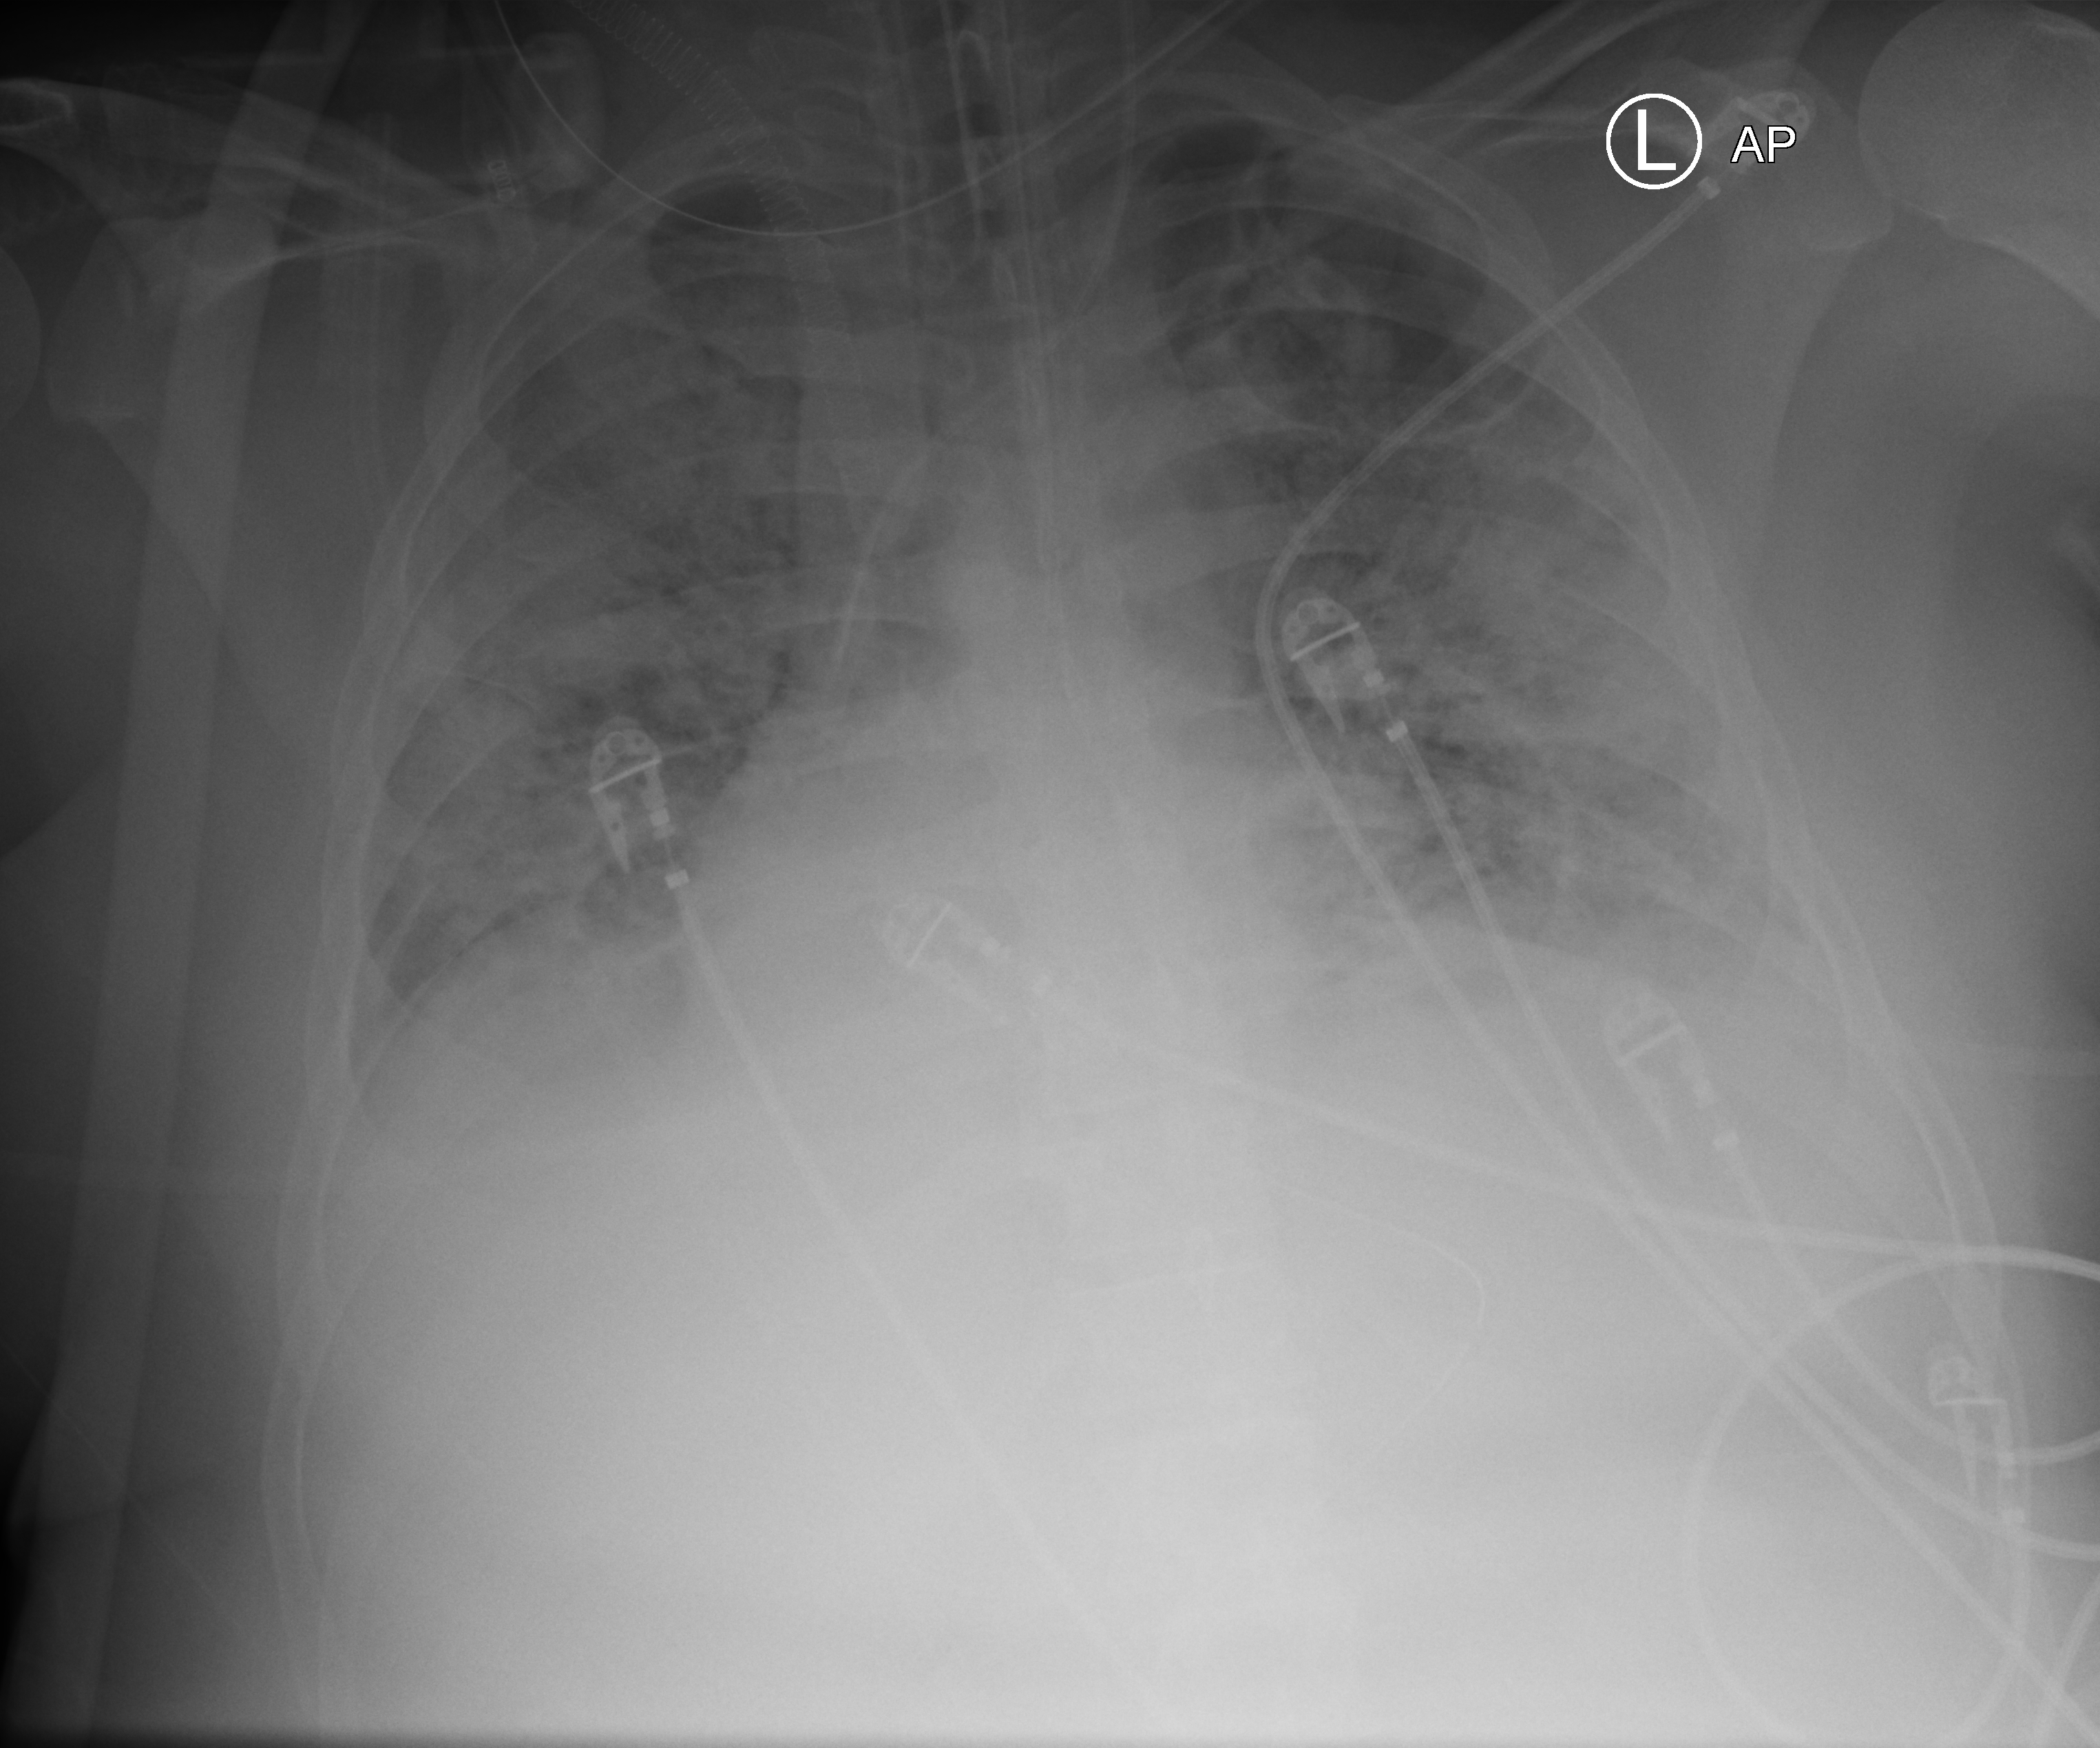
Portable chest radiograph; anteroposterior (AP) projection. Patient hospitalised with COVID-19, aged 18–59 years.
From the hospital-stay record, not from the radiograph (when in the stay this image was taken is not recorded): smoking status (admission record): never; length of hospital stay: 15 days.